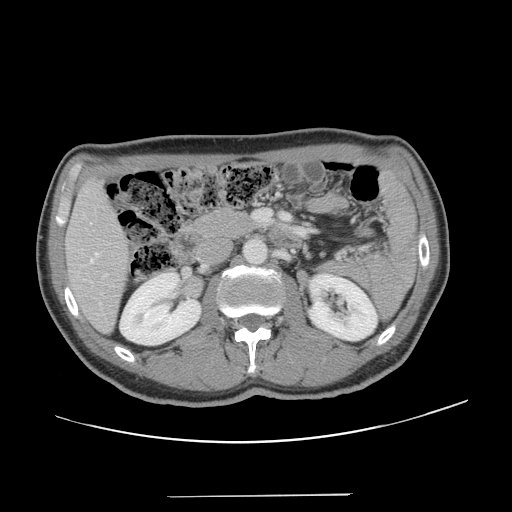
Contrast-enhanced abdominal CT, one axial slice; slice 61 of 131 in the series (ordered by position); intravenous contrast given; soft-tissue window (W 400 / L 40 HU); 2.5 mm slice thickness; 512 × 512 image matrix. Male patient, age 60 years. From the clinical record (not read from this slice): diagnosis: colorectal cancer liver metastases, imaged before liver resection; multiple liver metastases: no; largest metastasis: 2.5 cm; disease in both lobes: no.
Outlined on this slice (outlined manually by an expert reader):
- hepatic veins: bounding box (x1, y1, x2, y2) in pixels: (91, 253, 98, 263)
- liver: (67, 181, 127, 332)
- planned liver remnant (the part of the liver to remain after resection): (67, 182, 127, 332)